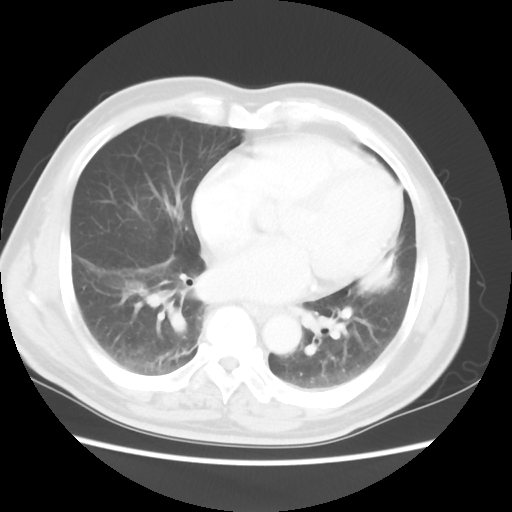
Chest CT, one axial slice; position 20 of 50 along the scan axis; reconstruction kernel STANDARD; lung window (W 1500 / L -600 HU); 5 mm slice thickness; 512 × 512 image matrix. Male patient, age 69 years. Case-level facts recorded for this patient, not image findings: clinical TNM (as recorded): T3 N1 M1a.
Structures marked on this image (rectangle marked by the reading radiologist):
- lung tumour (recorded histology: squamous cell carcinoma): bounding box <349,250,409,303> (left, top, right, bottom; pixels)